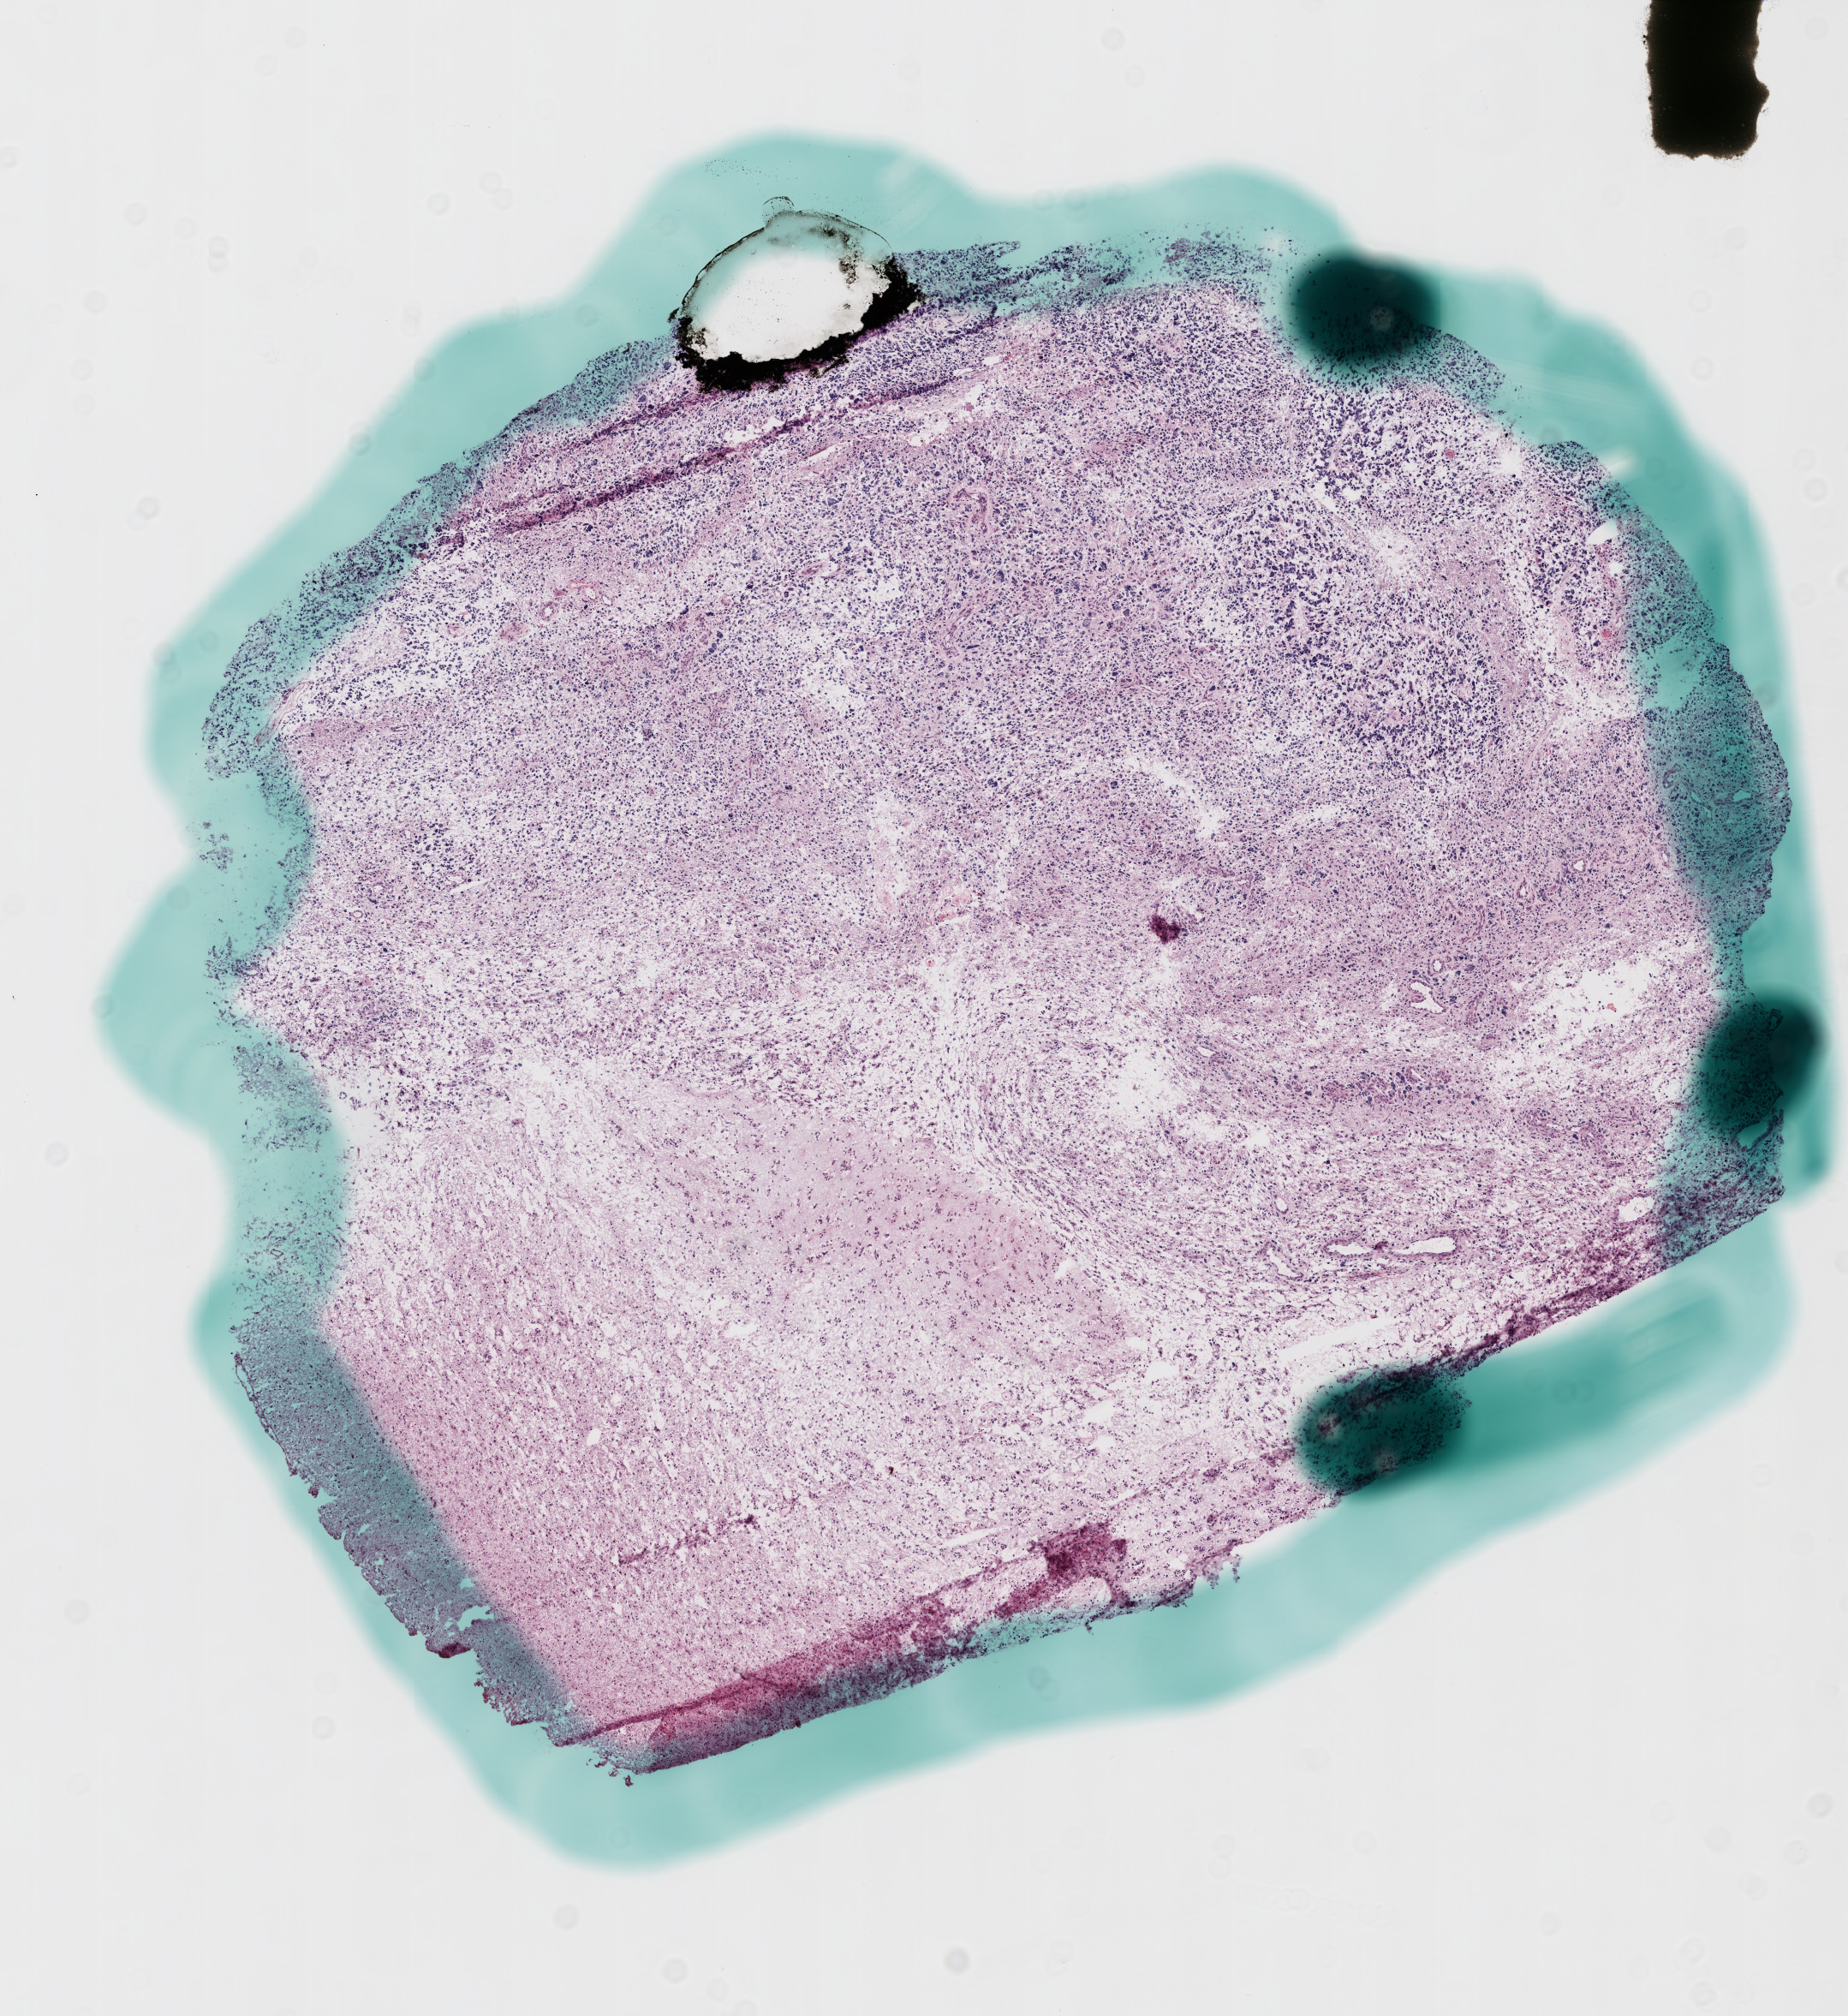
H&E whole-slide image, shown as a low-resolution overview of the whole scanned area (about 8.7 x 9.5 mm); frozen section from the bottom of the tissue portion; brain, primary tumour sample. Patient: male, age at initial diagnosis 71 years. Composition of this section per pathologist review: tumour cells 60%, tumour nuclei 95%, normal cells 0%, stromal cells 30%, necrosis 10%.
* histologic diagnosis: Glioblastoma